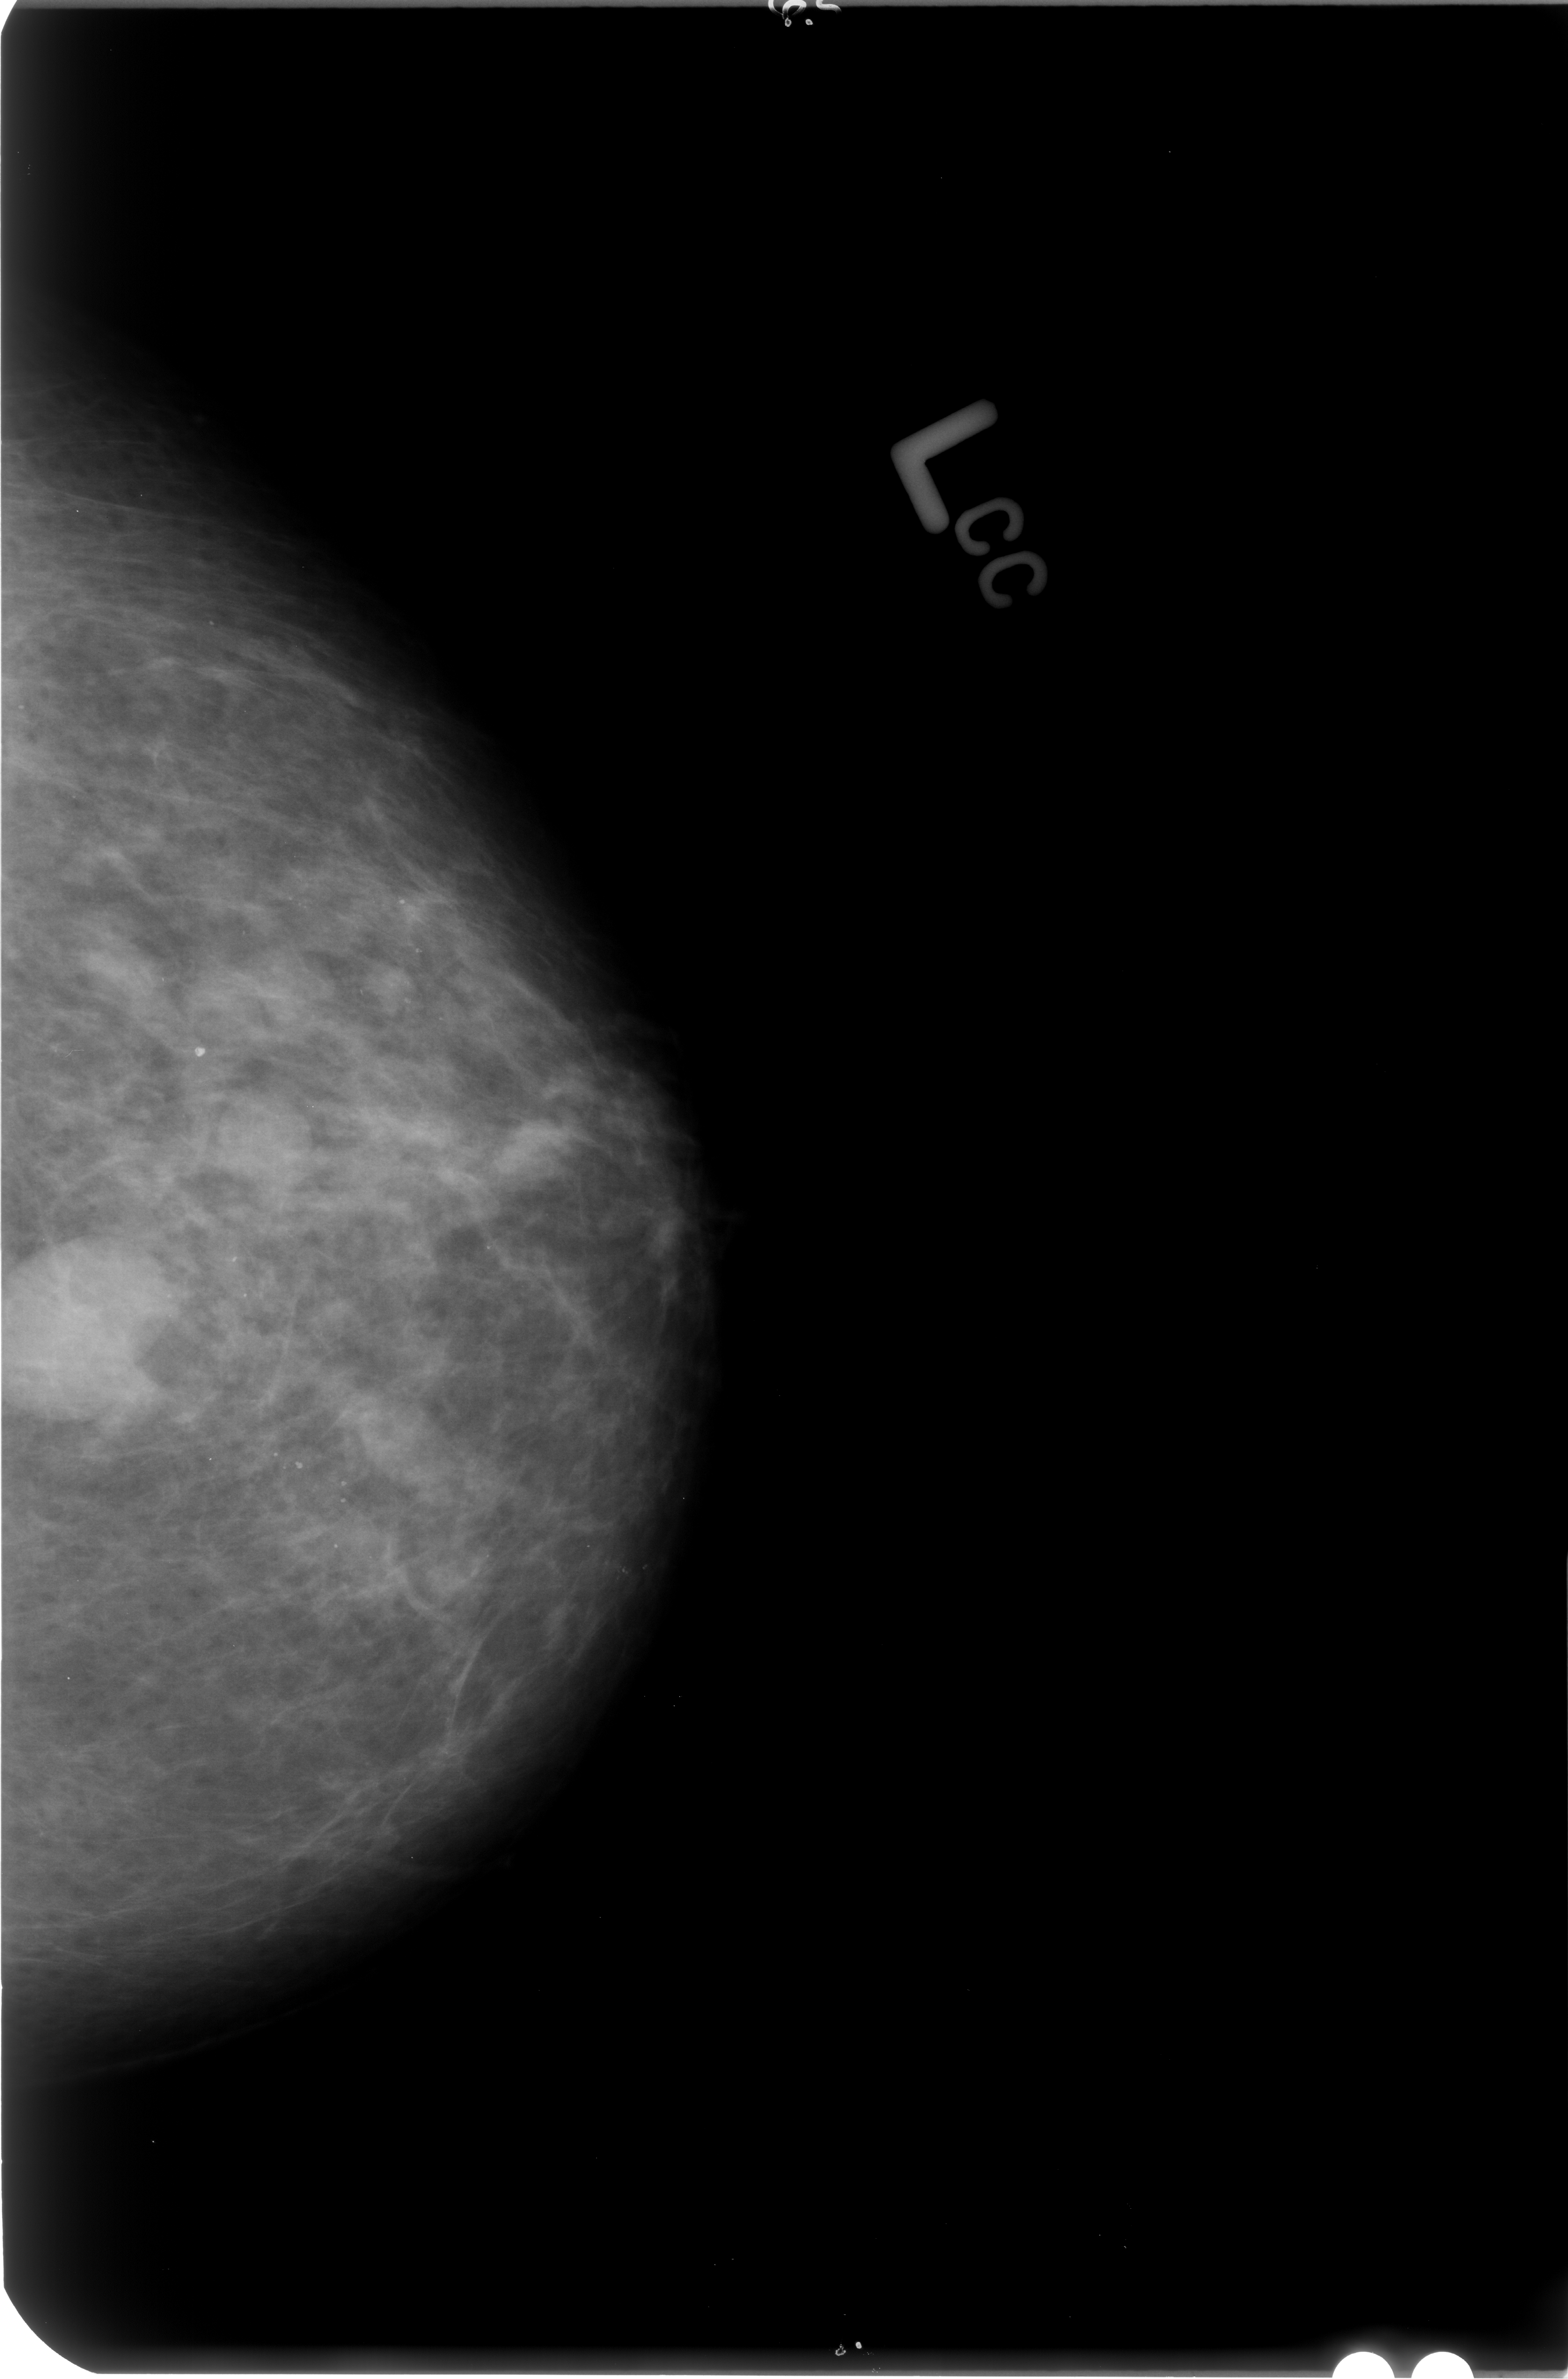
Mammogram (digitized film). Left breast. CC view. BI-RADS breast density category 2 (scale 1–4). 1568 × 2379 image matrix.
Marked abnormalities (boxes around the expert regions of interest):
- Finding 1 of 2: mass, shape round / oval, margins circumscribed / obscured; BI-RADS assessment category 4; pathology (as recorded): benign: bounding box <0,1213,157,1431> (left, top, right, bottom; pixels)
- Finding 2 of 2: mass, shape round / oval, margins circumscribed / obscured; BI-RADS assessment category 4; pathology (as recorded): benign: <193,1086,323,1207>